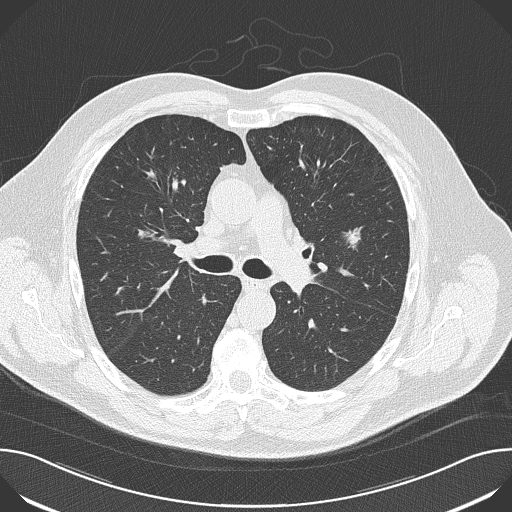
Low-dose screening chest CT, axial slice, first (baseline) screen, lung window (W 1500 / L -600 HU), 2 mm slice thickness, lung (sharp) reconstruction kernel (B50f), 120 kVp, slice 66 of 174 in the series, 512 × 512 image matrix, field of view 380 × 380 mm. Male participant, aged 65 years at enrolment. Former smoker at enrolment.
- Lesion marked by an expert reader, bounding box (x1, y1, x2, y2) in pixels: (331, 221, 373, 262).
- The screening reader recorded 5 non-calcified nodules or masses ≥4 mm on this exam (left upper lobe, left upper lobe, left upper lobe, right upper lobe, right middle lobe); which of them this box marks is not recorded.
- Official screen result: positive, change unspecified: nodule(s) >= 4 mm or enlarging nodule(s), mass(es), or other non-specific abnormalities suspicious for lung cancer.
- Later outcome: lung cancer diagnosed 52 days after this screen — adenocarcinoma, NOS, left upper lobe, moderately differentiated (G2), stage IA (AJCC 6th edition), 10 mm at pathology.